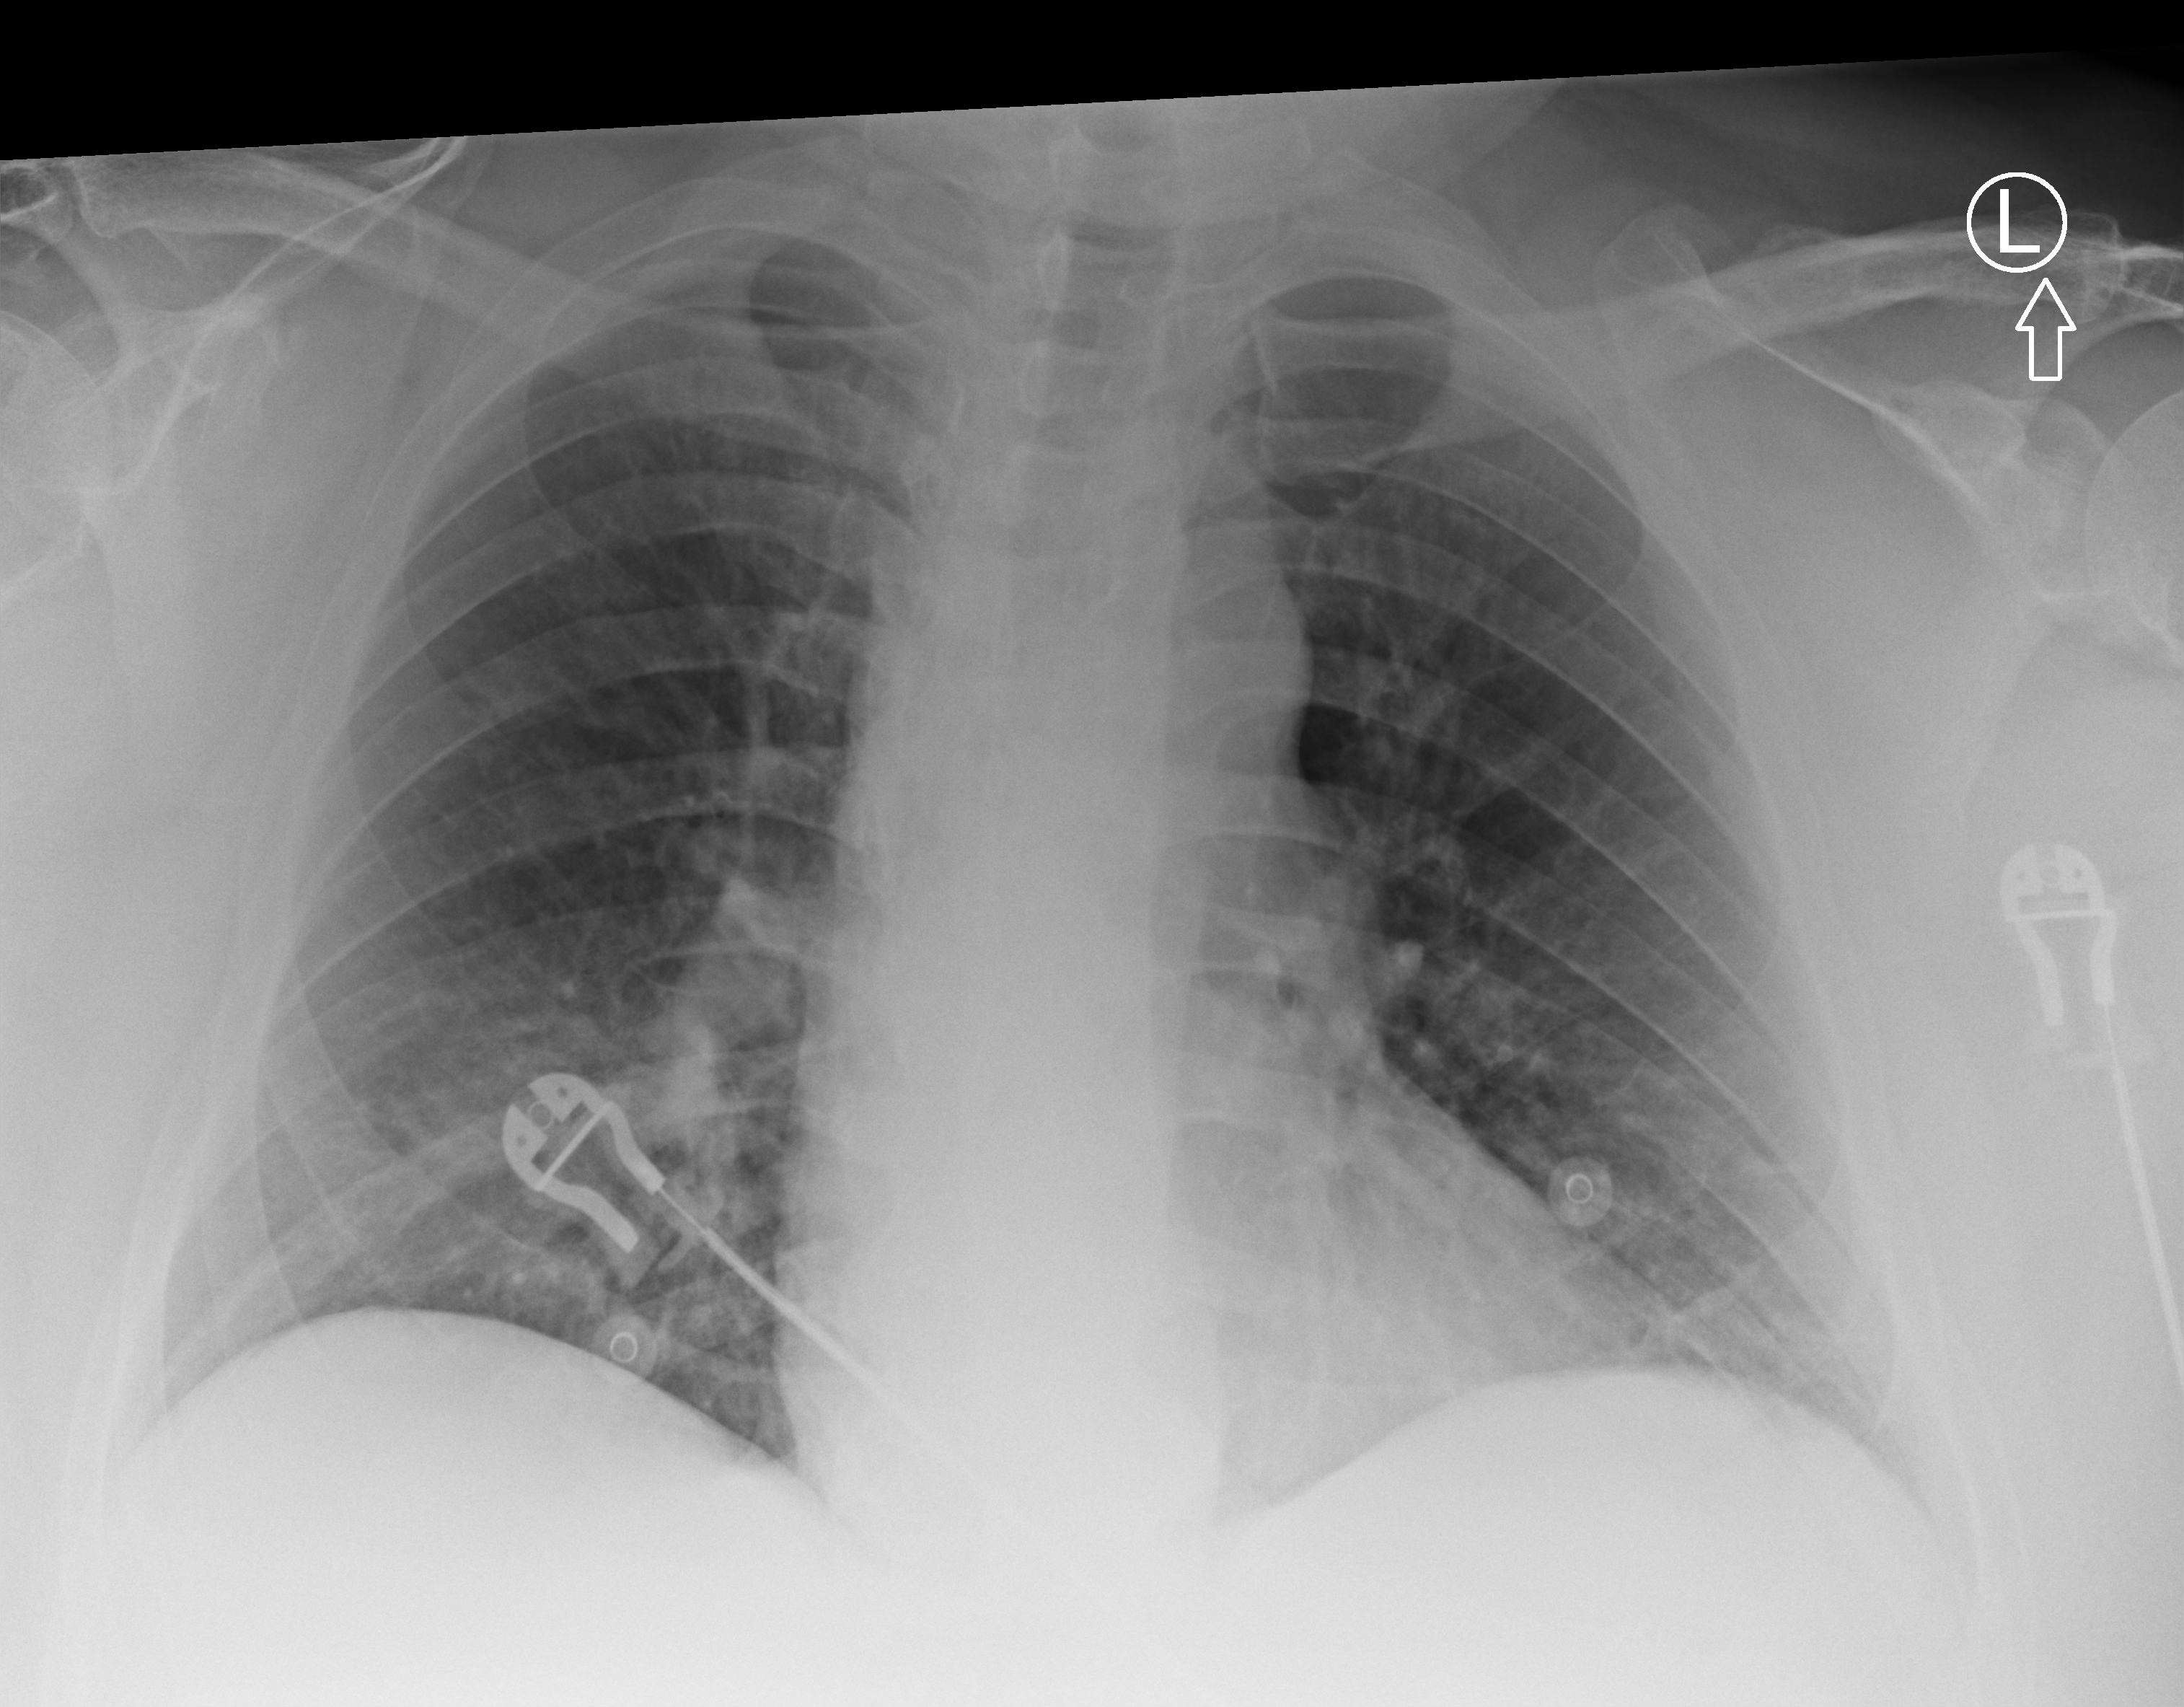
Chest X-ray (portable). Patient hospitalised with COVID-19; male, aged 18–59 years.
Admission-level facts for this patient (not findings on this image; timing relative to this image not recorded):
- mechanically ventilated during this hospital stay: no
- length of hospital stay: 25 days
- admitted to intensive care during this hospital stay: no